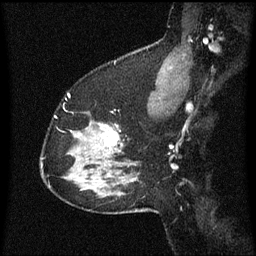
Breast MRI (dynamic contrast-enhanced), one sagittal slice; dynamic contrast-enhanced series, image 2 of 3 at this slice position (ordered by acquisition); 1.5 T; TE 4.2 ms, TR 8.4 ms; 2 mm slice thickness; 256 × 256 image matrix, field of view 200 × 200 mm. Female patient, age 37 years. Case-level facts recorded for this patient, not image findings: setting: breast cancer imaged before/during neoadjuvant chemotherapy; receptor status: HR-positive, HER2-negative.
Outlined on this slice (semi-automatic segmentation, software-assisted and operator-edited):
- analysis volume of interest (the breast-tissue region the enhancement analysis was run in; not a lesion): bounding box [x1, y1, x2, y2] px = [94, 122, 125, 157]
- tumour enhancement mask (voxels above the 70 % enhancement threshold inside the analysis volume of interest): [102, 126, 123, 147]